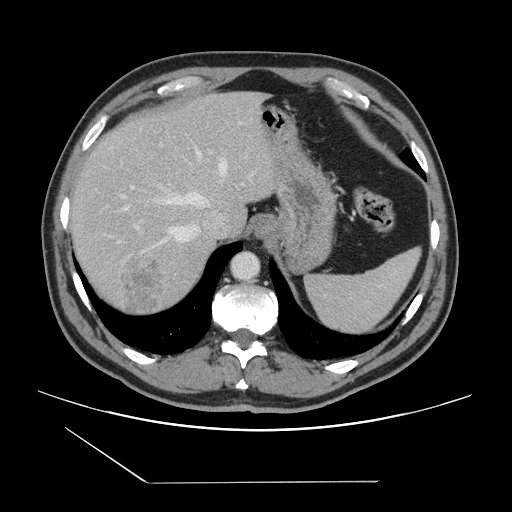
Contrast-enhanced abdominal CT, one axial slice. Slice 116 of 157 in the series (ordered by position). Intravenous contrast given. Soft-tissue window (W 400 / L 40 HU). 2.5 mm slice thickness. 512 × 512 image matrix, field of view 407 × 407 mm. Male patient, age 61 years. From the clinical record (not read from this slice): diagnosis: colorectal cancer liver metastases, imaged before liver resection; multiple liver metastases: yes; largest metastasis: 5.5 cm.
Structures marked on this image (manually delineated by an expert):
- hepatic veins: box from (x=121, y=151) to (x=227, y=253) px
- liver: (x=70, y=92)–(x=277, y=315)
- planned liver remnant (the part of the liver to remain after resection): (x=71, y=93)–(x=235, y=231)
- portal vein (with intrahepatic branches): (x=131, y=186)–(x=140, y=231)
- liver metastasis: (x=120, y=250)–(x=168, y=316)